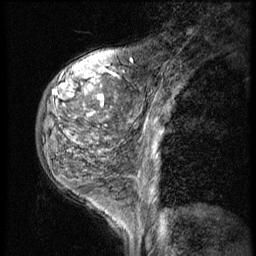
Breast MRI (dynamic contrast-enhanced), one sagittal slice. Position 15 of 56 along the scan axis. 3 images stored at this slice position (order not interpretable as contrast timing). 1.5 T. TE 4.2 ms, TR 9 ms. 2.5 mm slice thickness. 256 × 256 image matrix, field of view 180 × 180 mm. Patient: female, 50 years. Case-level facts recorded for this patient, not image findings: setting: breast cancer imaged before/during neoadjuvant chemotherapy; receptor status: triple-negative.
Outlined on this slice (semi-automatically segmented with operator editing):
- analysis volume of interest (the breast-tissue region the enhancement analysis was run in; not a lesion): bounding box (x1, y1, x2, y2) in pixels: (35, 50, 116, 191)
- tumour enhancement mask (voxels above the 140 % enhancement threshold inside the analysis volume of interest): (53, 85, 102, 116)